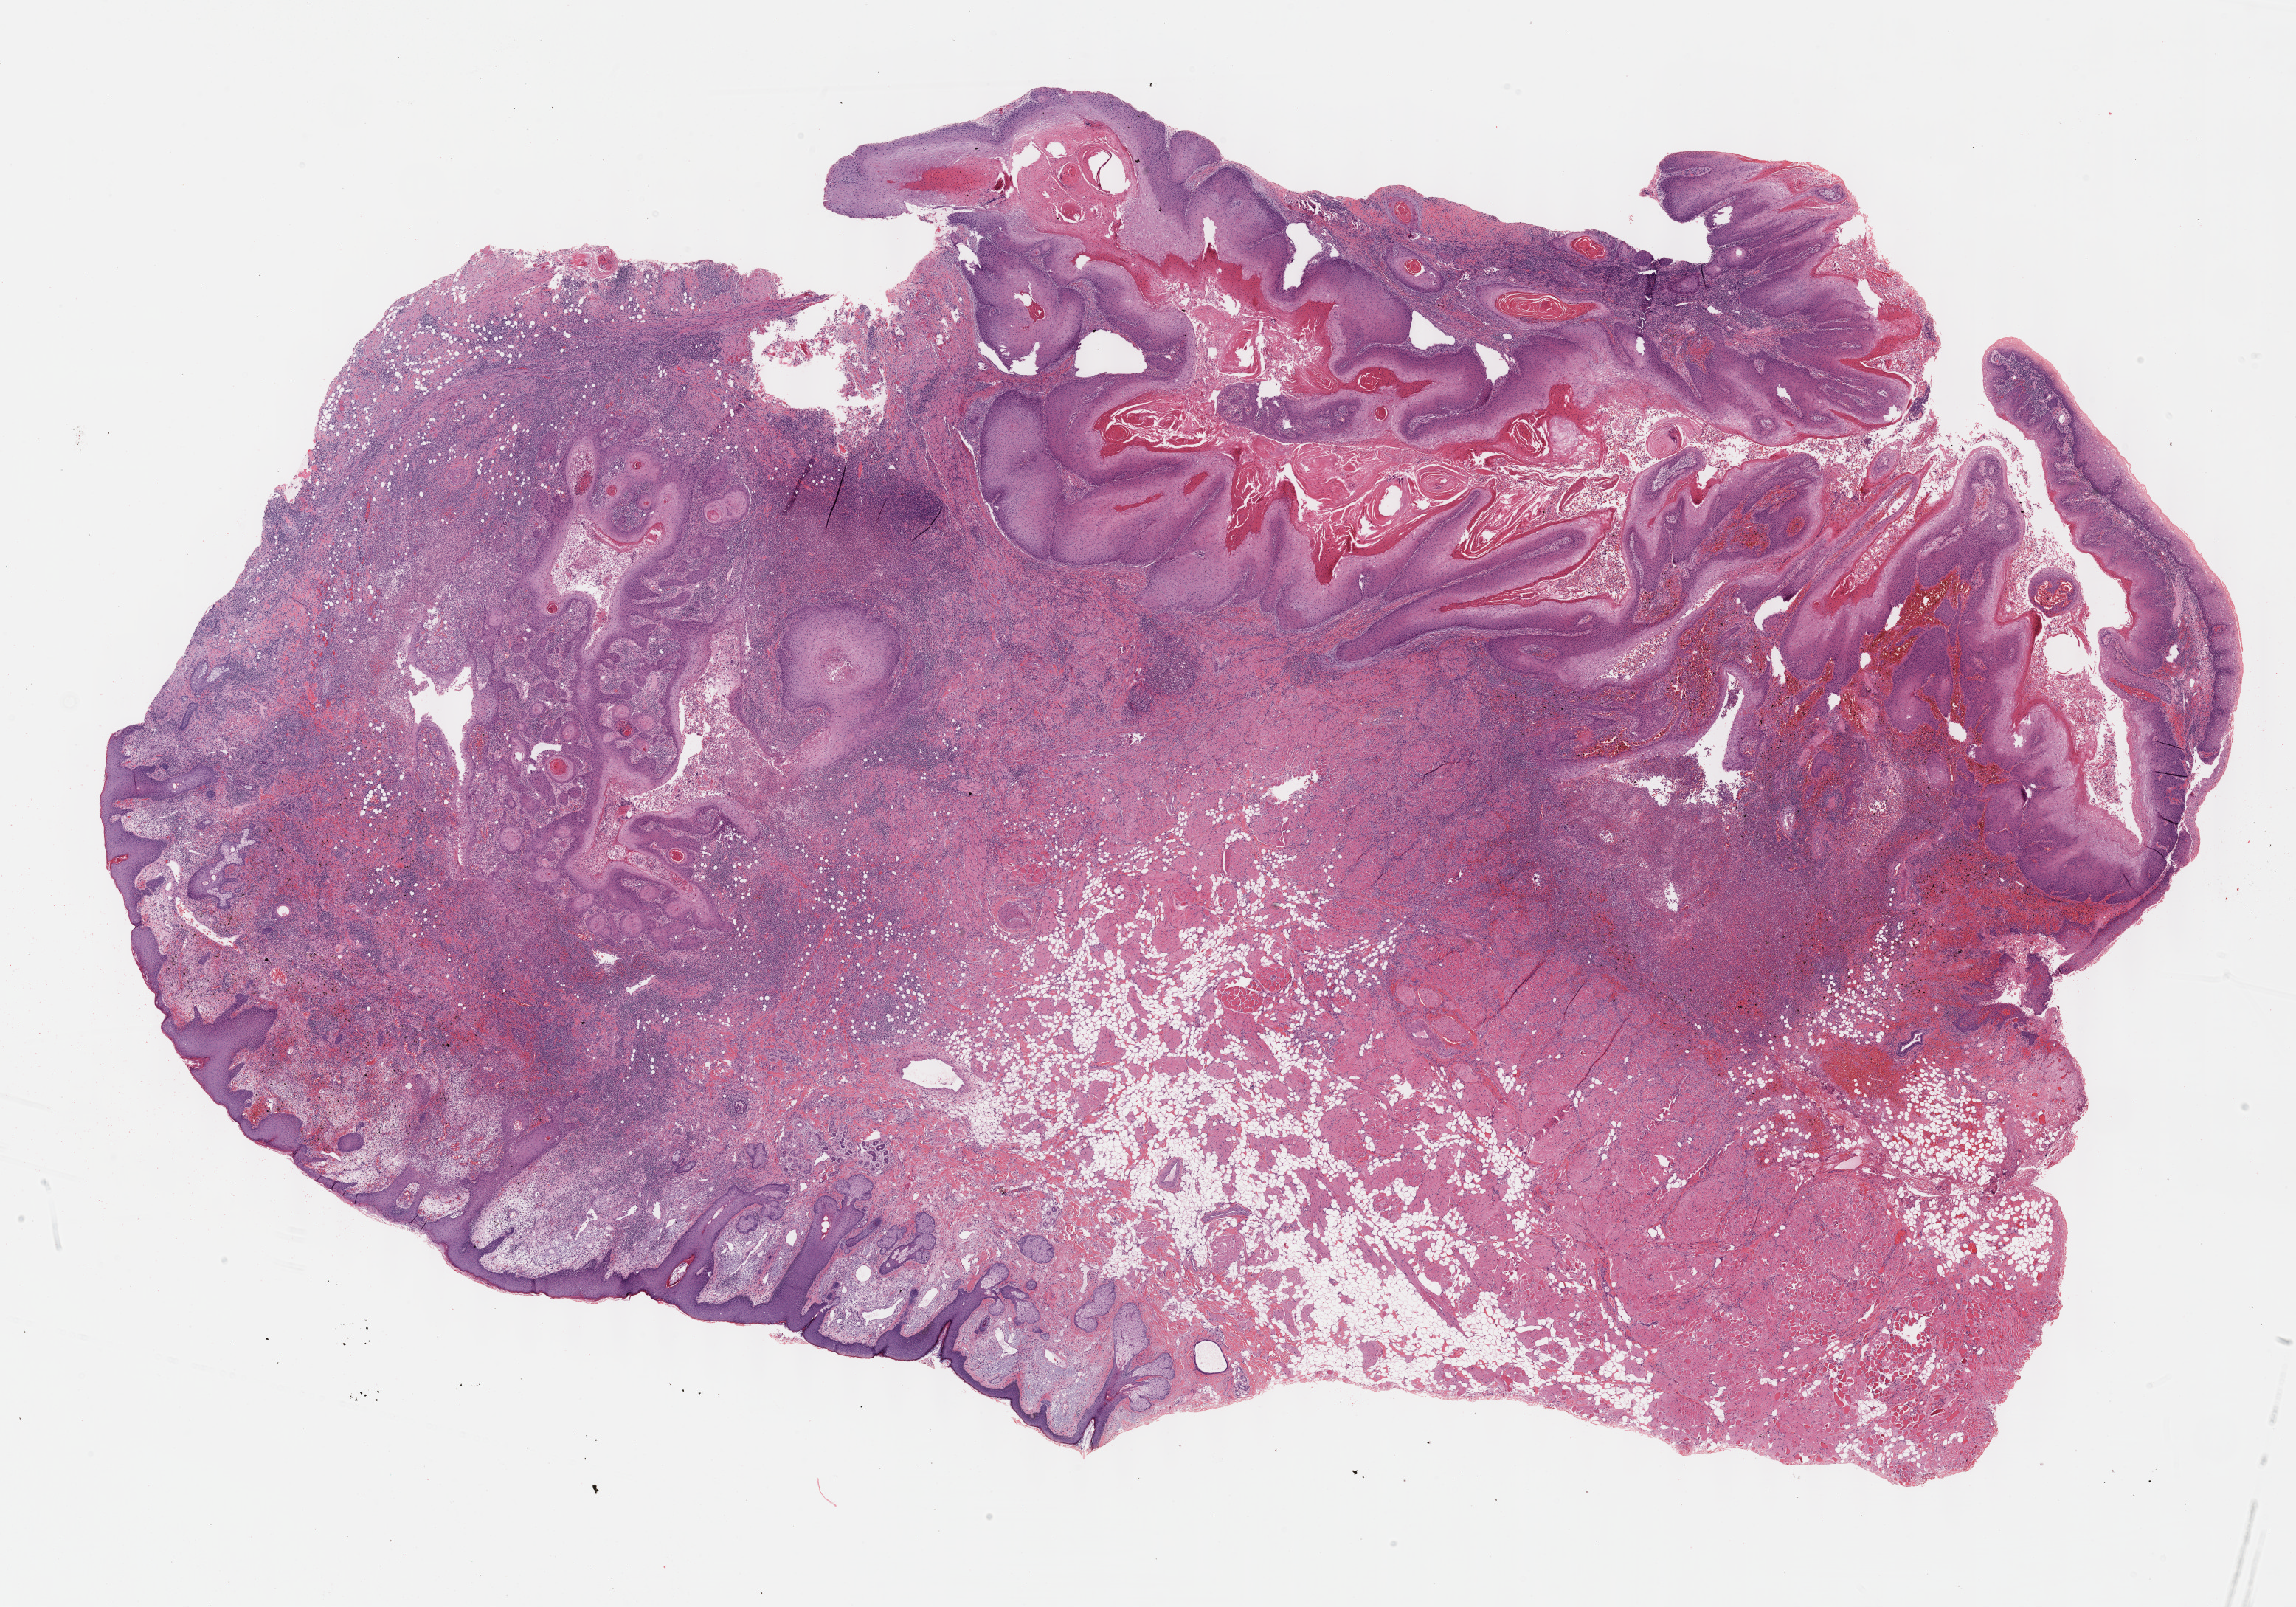
Whole-slide histology image, H&E — low-resolution overview of the scanned area, about 25.1 x 17.6 mm, FFPE section, sample: primary tumour, head and neck. Patient: female, age at initial diagnosis 82 years. Histologic grade: G2 (moderately differentiated).
Diagnosis: Squamous cell carcinoma, NOS (floor of mouth, NOS). AJCC pathologic stage: IVA (6th edition). TNM: T4a N0 M0.